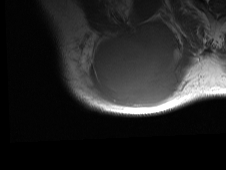
MRI of an extremity soft-tissue mass, one axial slice. Slice 53 of 81 in the series (ordered by position). MR volume resampled by the dataset authors to the PET/CT grid (not the native acquisition matrix). 3.27 mm slice thickness. 226 × 170 image matrix. Male patient. Case-level facts recorded for this patient, not image findings: histological type: pleiomorphic spindle cell undifferentiated; grade: high; site of the primary tumour: right parascapusular.
Outlined on this slice (expert contour drawn on MRI and transferred to this co-registered scan by the dataset authors):
- gross tumour volume including surrounding oedema: box from (x=71, y=24) to (x=195, y=112) px
- gross tumour volume (mass): (x=92, y=27)–(x=179, y=107)